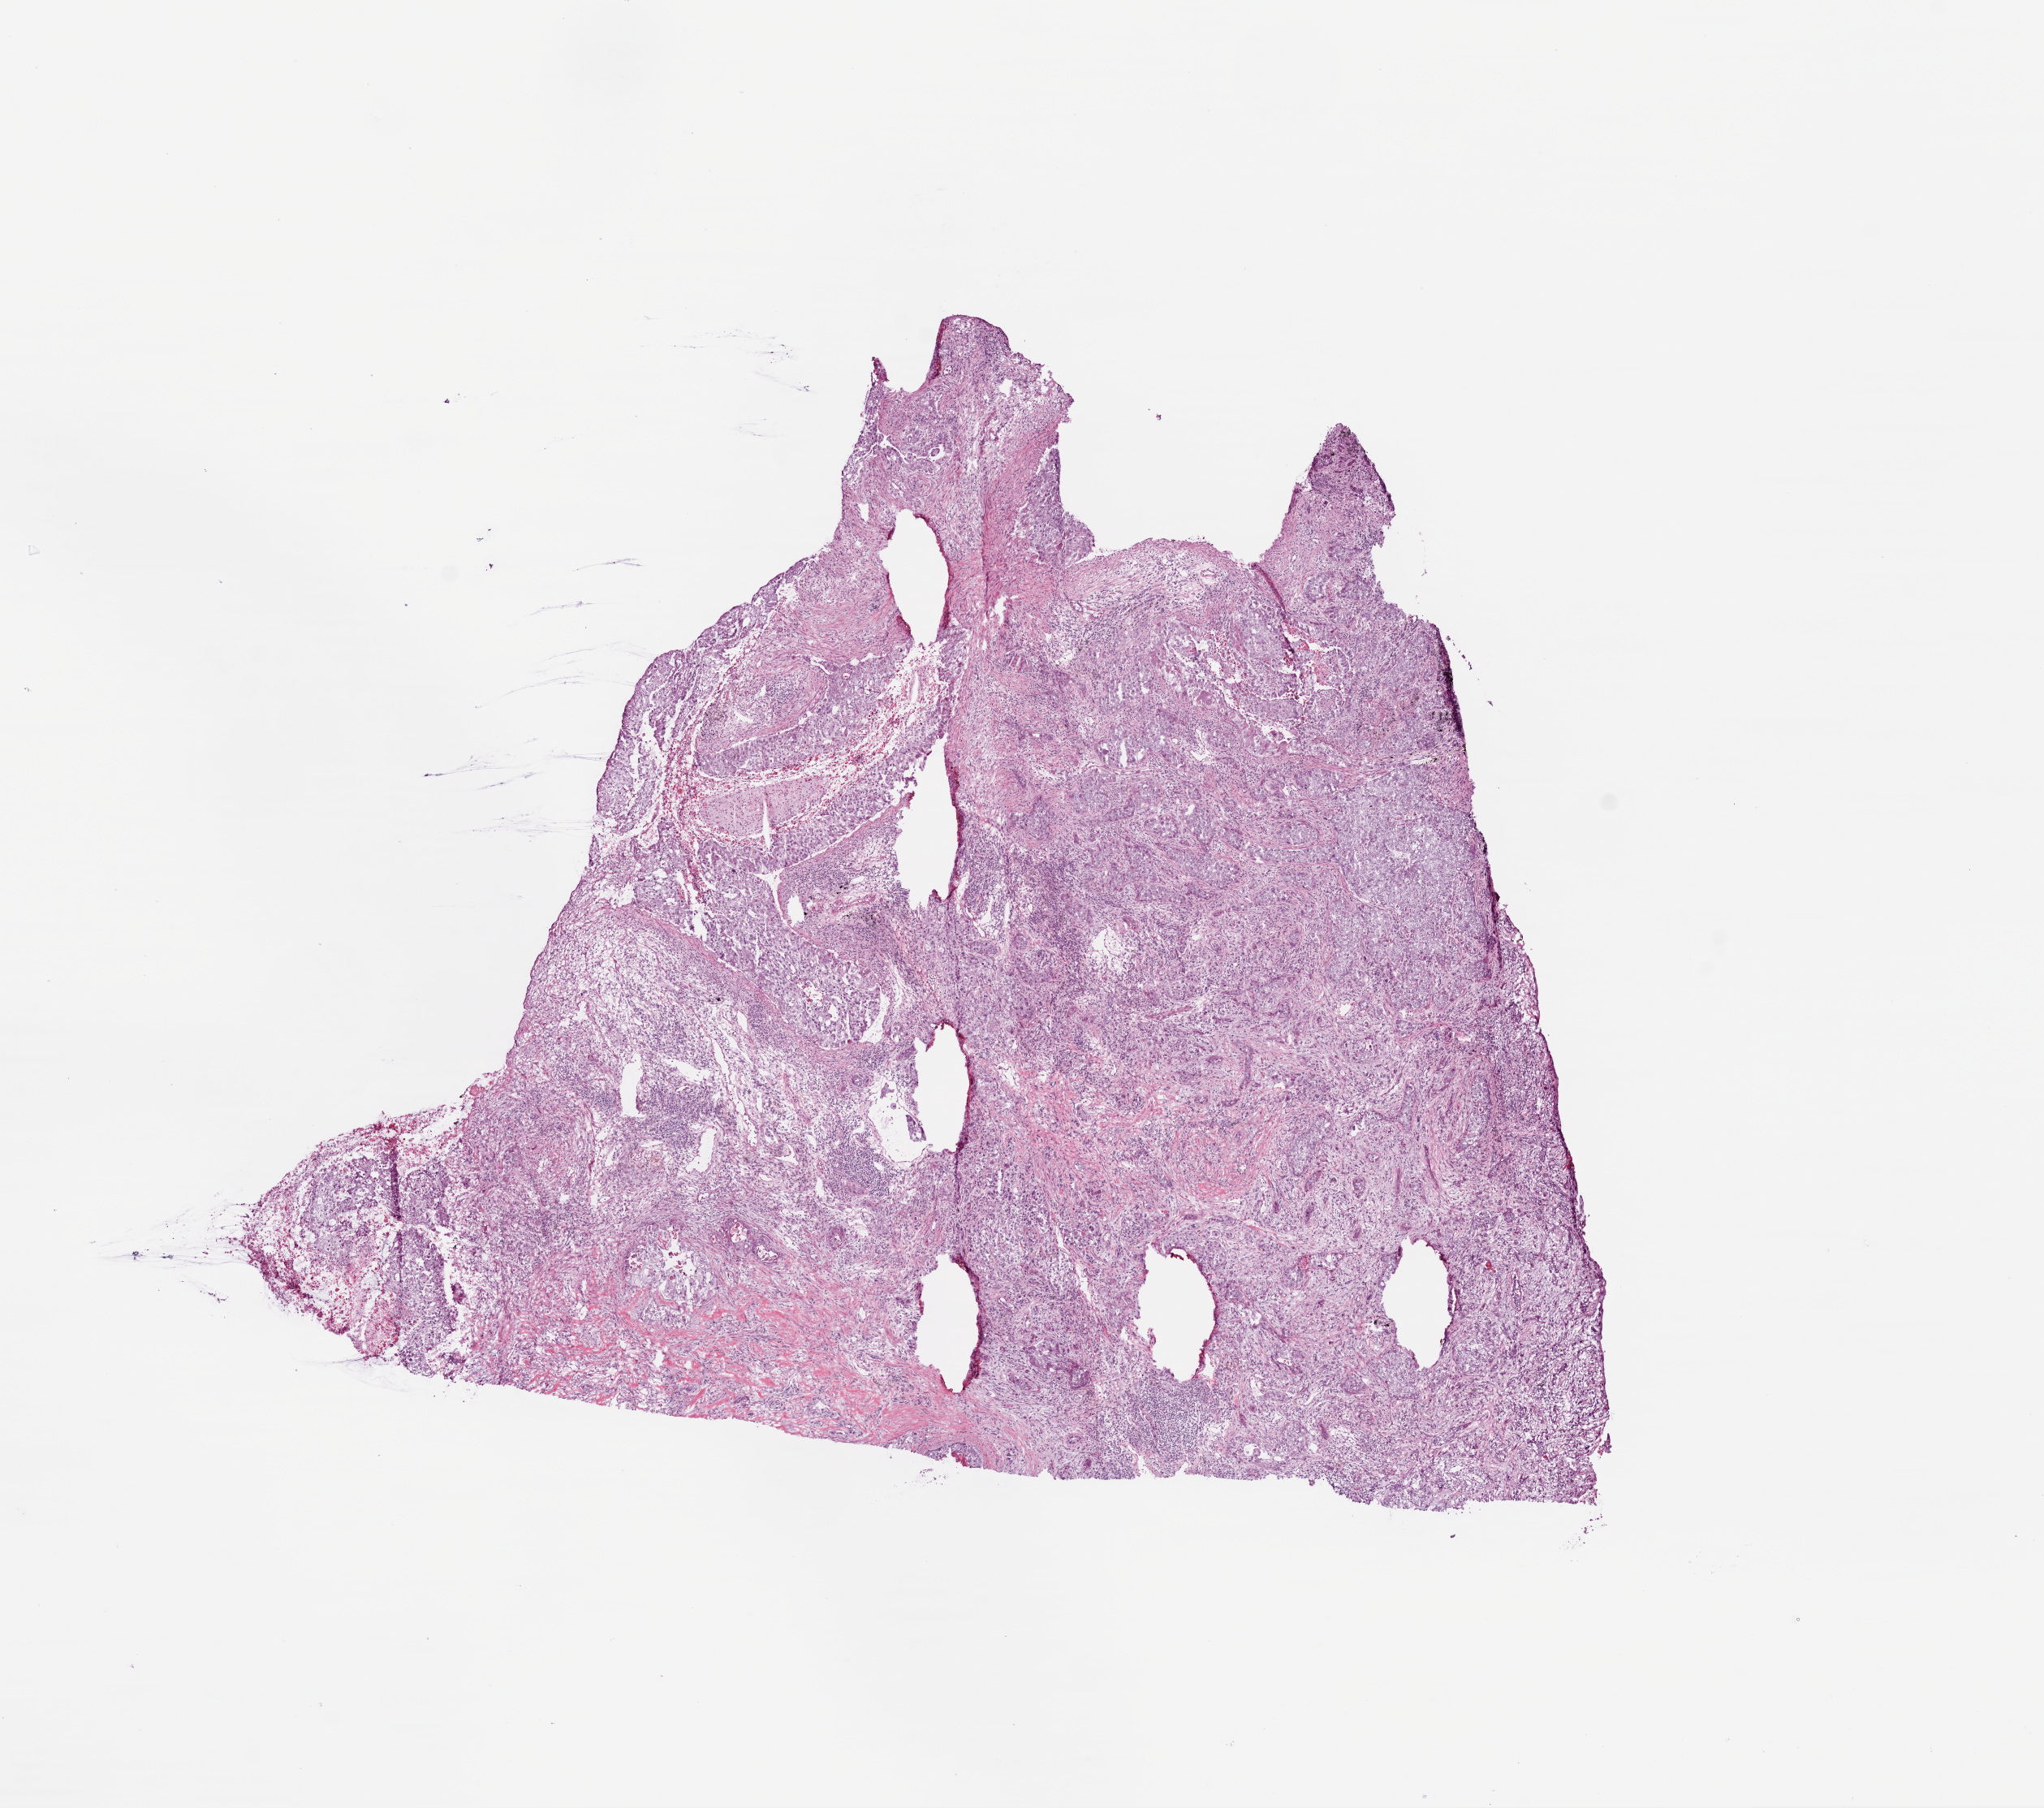
Digitized H&E-stained tissue section (whole slide) — whole scanned area (about 10.2 x 9.0 mm, acquisition: 20x scan) shown as a low-resolution overview, frozen section from the top of the tissue portion, lung, primary tumour sample. Male patient; age at initial diagnosis 61 years. Pathologist review of this section (percent, as recorded): tumour cells 85%, tumour nuclei 65%.
Pathologic diagnosis: Adenocarcinoma with mixed subtypes (lower lobe, lung).